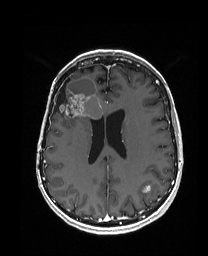
Brain MRI from a brain-tumour surgery series, one axial slice. T1-weighted post-contrast. 208 × 256 image matrix, field of view 203 × 250 mm. Case-level facts recorded for this patient, not image findings: histopathology: Metastatic Carcinoma from Breast primary.
Outlined on this slice (expert manual segmentation):
- previous resection cavity: bounding box (x1, y1, x2, y2) in pixels: (53, 78, 70, 112)
- tumour: (55, 77, 104, 128)